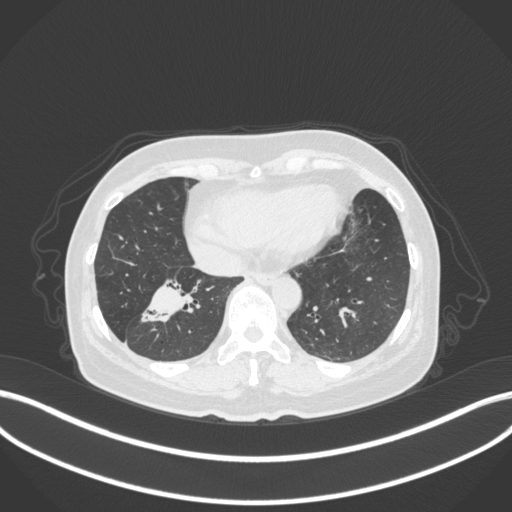
Chest CT, one axial slice. Slice 121 of 429 in the series (ordered by position). Reconstruction kernel B31f. 120 kVp. Lung window (W 1500 / L -600 HU). 1 mm slice thickness. 512 × 512 image matrix. Female patient, age 67 years. Case-level facts recorded for this patient, not image findings: clinical TNM (as recorded): T1c N1 M0; histopathological grade: G2-3.
Outlined on this slice (bounding box drawn by a radiologist):
- lung tumour (recorded histology: adenocarcinoma): bounding box (x1, y1, x2, y2) in pixels: (137, 272, 206, 332)